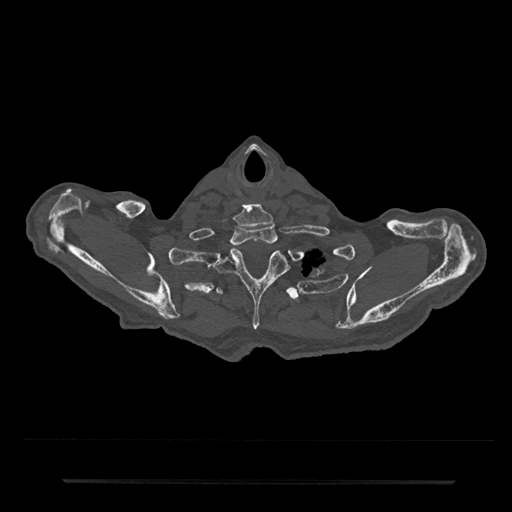
CT including the spine, one axial slice; 120 kVp; bone window (W 1800 / L 400 HU); 0.5 mm slice thickness; 512 × 512 image matrix, field of view 427 × 427 mm. Male patient, age 74 years. From the clinical record (not read from this slice): primary cancer: prostate.
Annotated regions visible in this slice (semi-automatically segmented with operator editing):
- T1 vertebra: bounding box (x1, y1, x2, y2) in pixels: (231, 225, 278, 245)
- T2 vertebra: (212, 249, 287, 330)
- T3 vertebra: (215, 286, 300, 301)